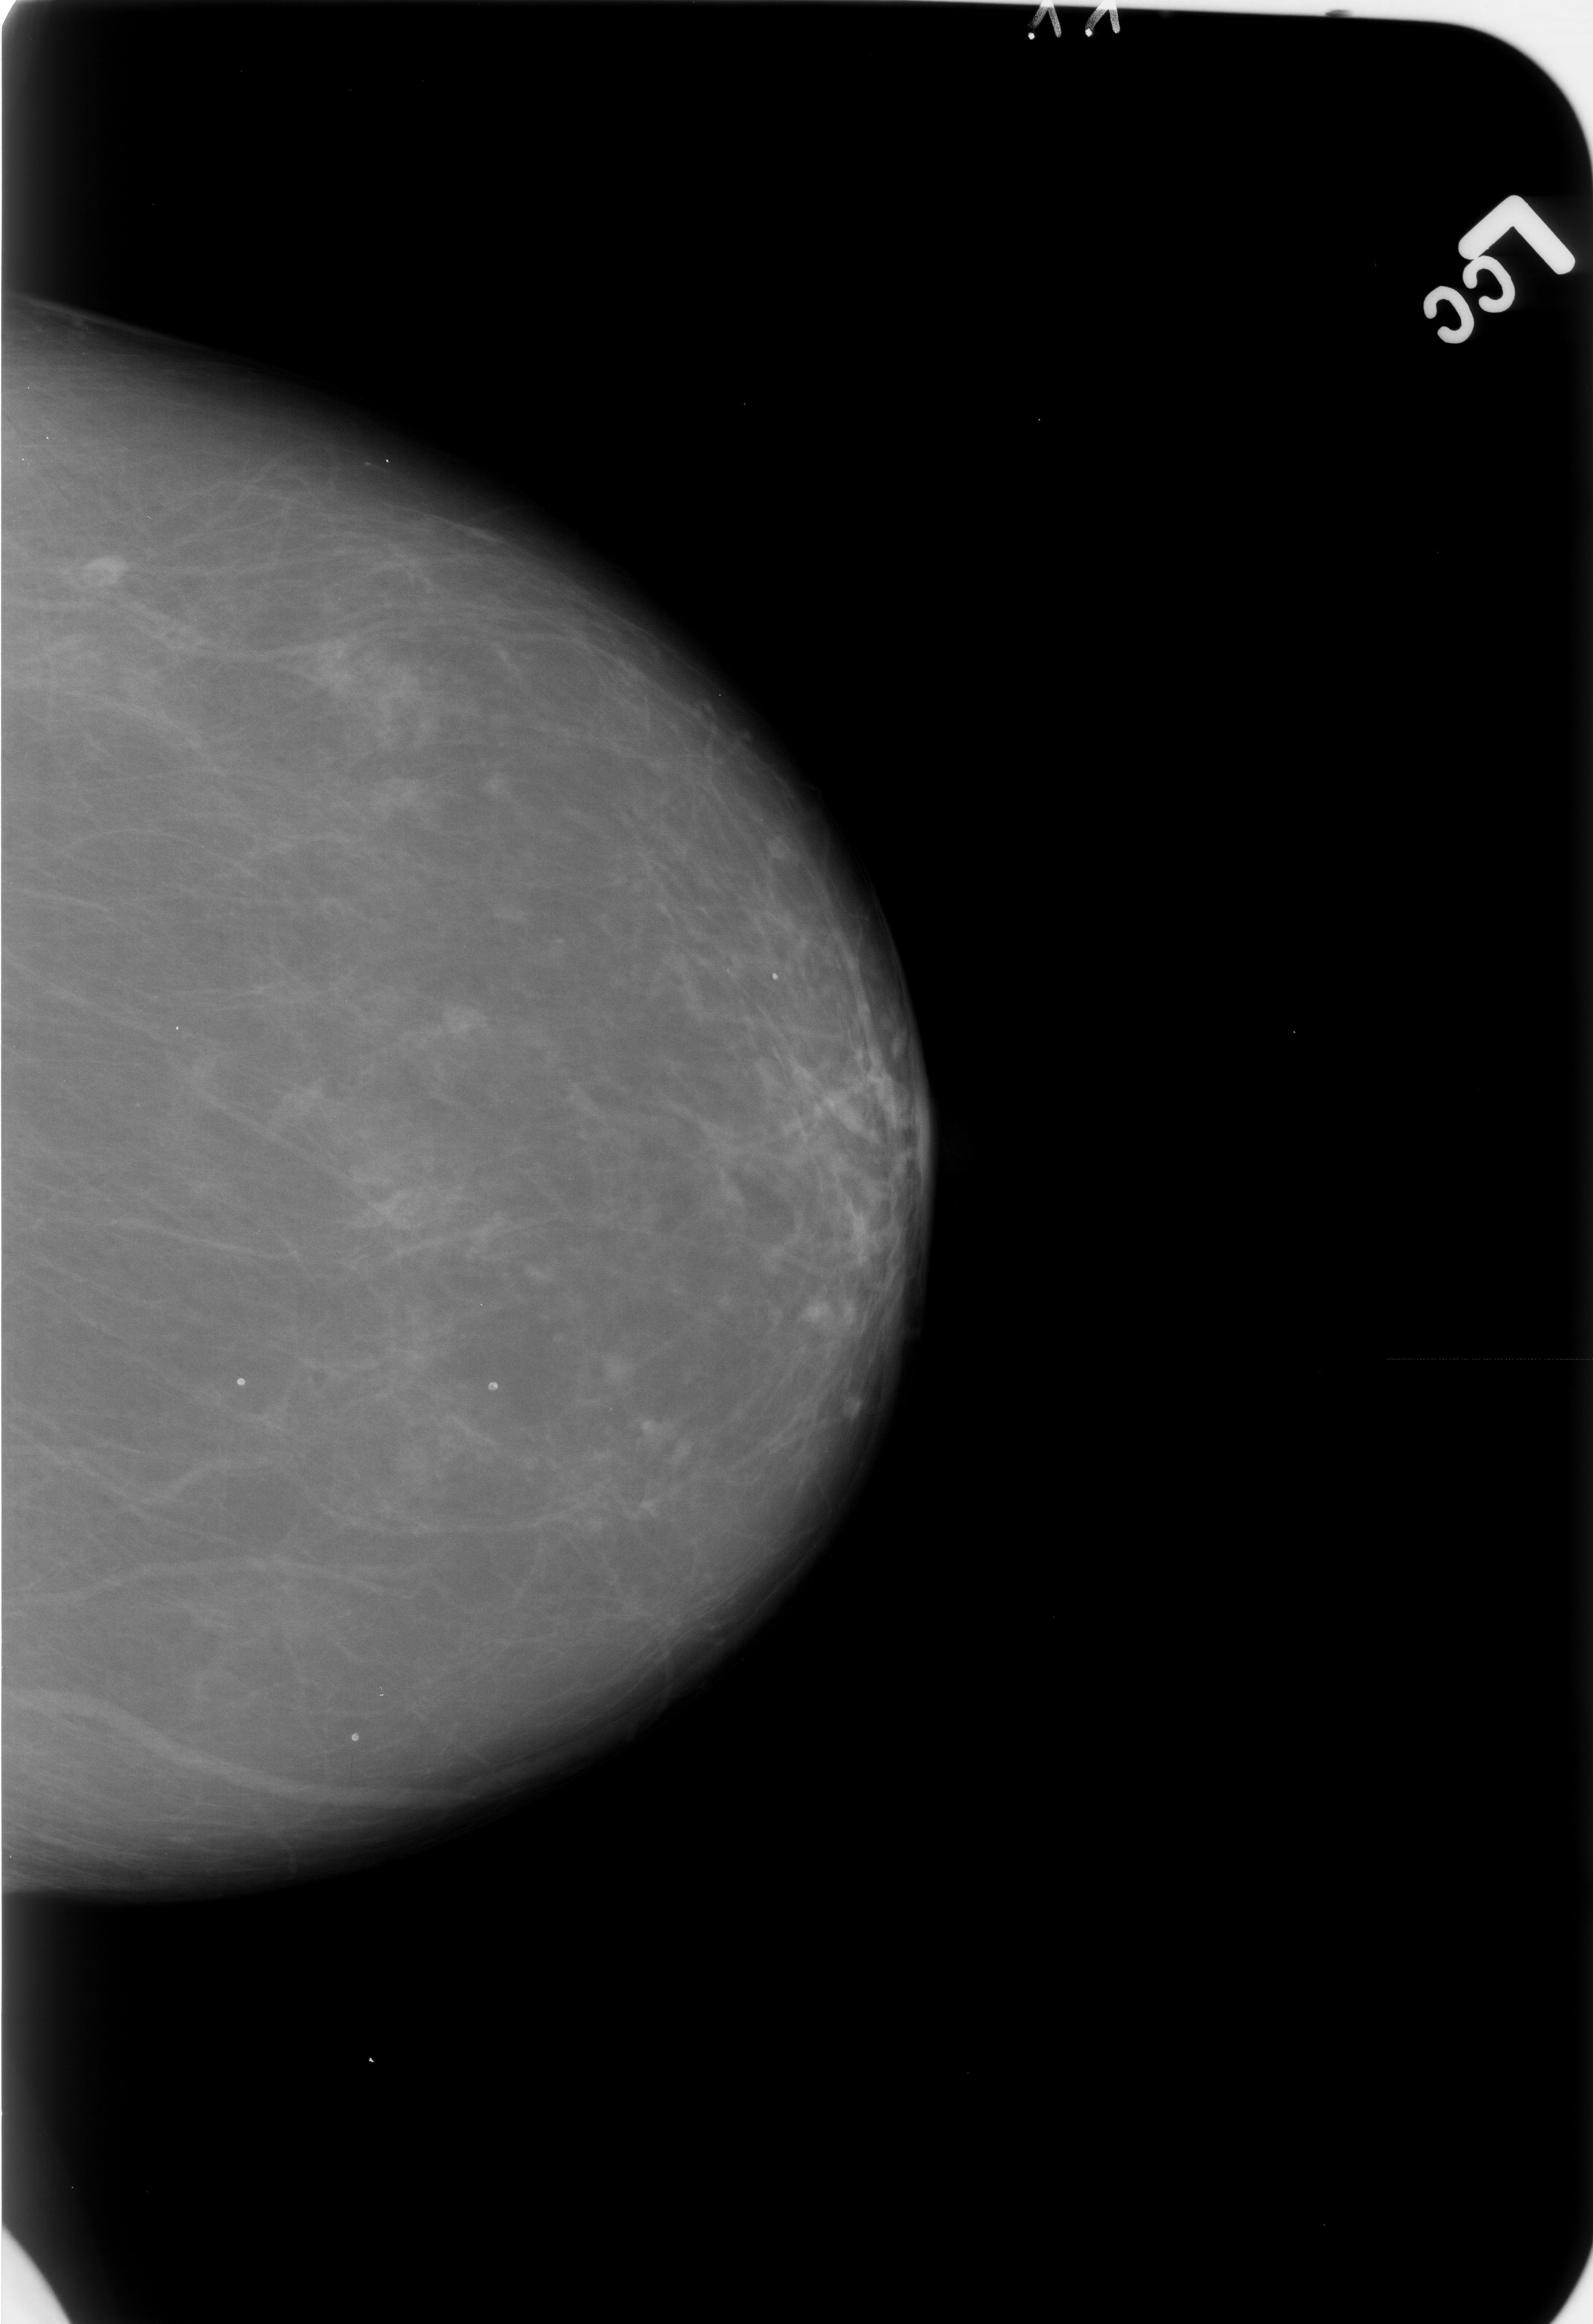
Digitized screen-film mammogram; left breast; CC view; BI-RADS breast density category 1 (scale 1–4).
Abnormality record for this image: Finding 1 of 4: calcifications, morphology lucent centered; BI-RADS assessment category 2; benign without callback (not worked up further). Finding 2 of 4: calcifications, morphology lucent centered; BI-RADS assessment category 2; subtlety rating 3 on a 1 (subtle) to 5 (obvious) scale; benign; no additional work-up was recommended (benign without callback). Finding 3 of 4: calcifications, morphology lucent centered; BI-RADS assessment category 2; benign; no additional work-up was recommended (benign without callback). Finding 4 of 4: calcifications, morphology lucent centered; BI-RADS assessment category 2; subtlety rating 3 on a 1 (subtle) to 5 (obvious) scale; benign; no additional work-up was recommended (benign without callback).